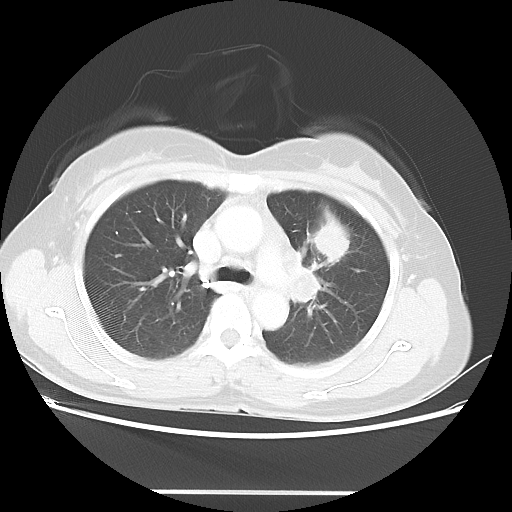
Chest CT, one axial slice. Lung window (W 1500 / L -600 HU). 5 mm slice thickness. 512 × 512 image matrix, field of view 360 × 360 mm. Patient: female, 50 years. From the clinical record (not read from this slice): clinical TNM (as recorded): T1c N1 M0; histopathological grade: G3.
Outlined on this slice (rectangle marked by the reading radiologist):
- lung tumour (recorded histology: adenocarcinoma): bounding box <308,210,350,265> (left, top, right, bottom; pixels)